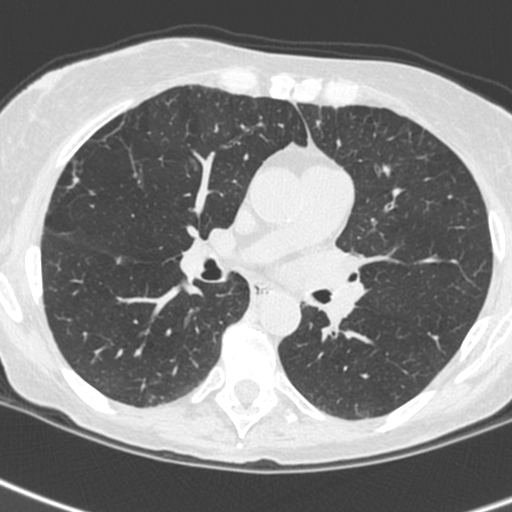
Low-dose screening chest CT, one axial slice. Position 138 of 242 along the scan axis. Lung window (W 1500 / L -600 HU). 1.3 mm slice thickness. 512 × 512 image matrix, field of view 284 × 284 mm.
Annotated regions visible in this slice (expert manual segmentation):
- lesion 3 (tumor, upper lobe of left lung): bounding box (x1, y1, x2, y2) in pixels: (301, 244, 365, 325)